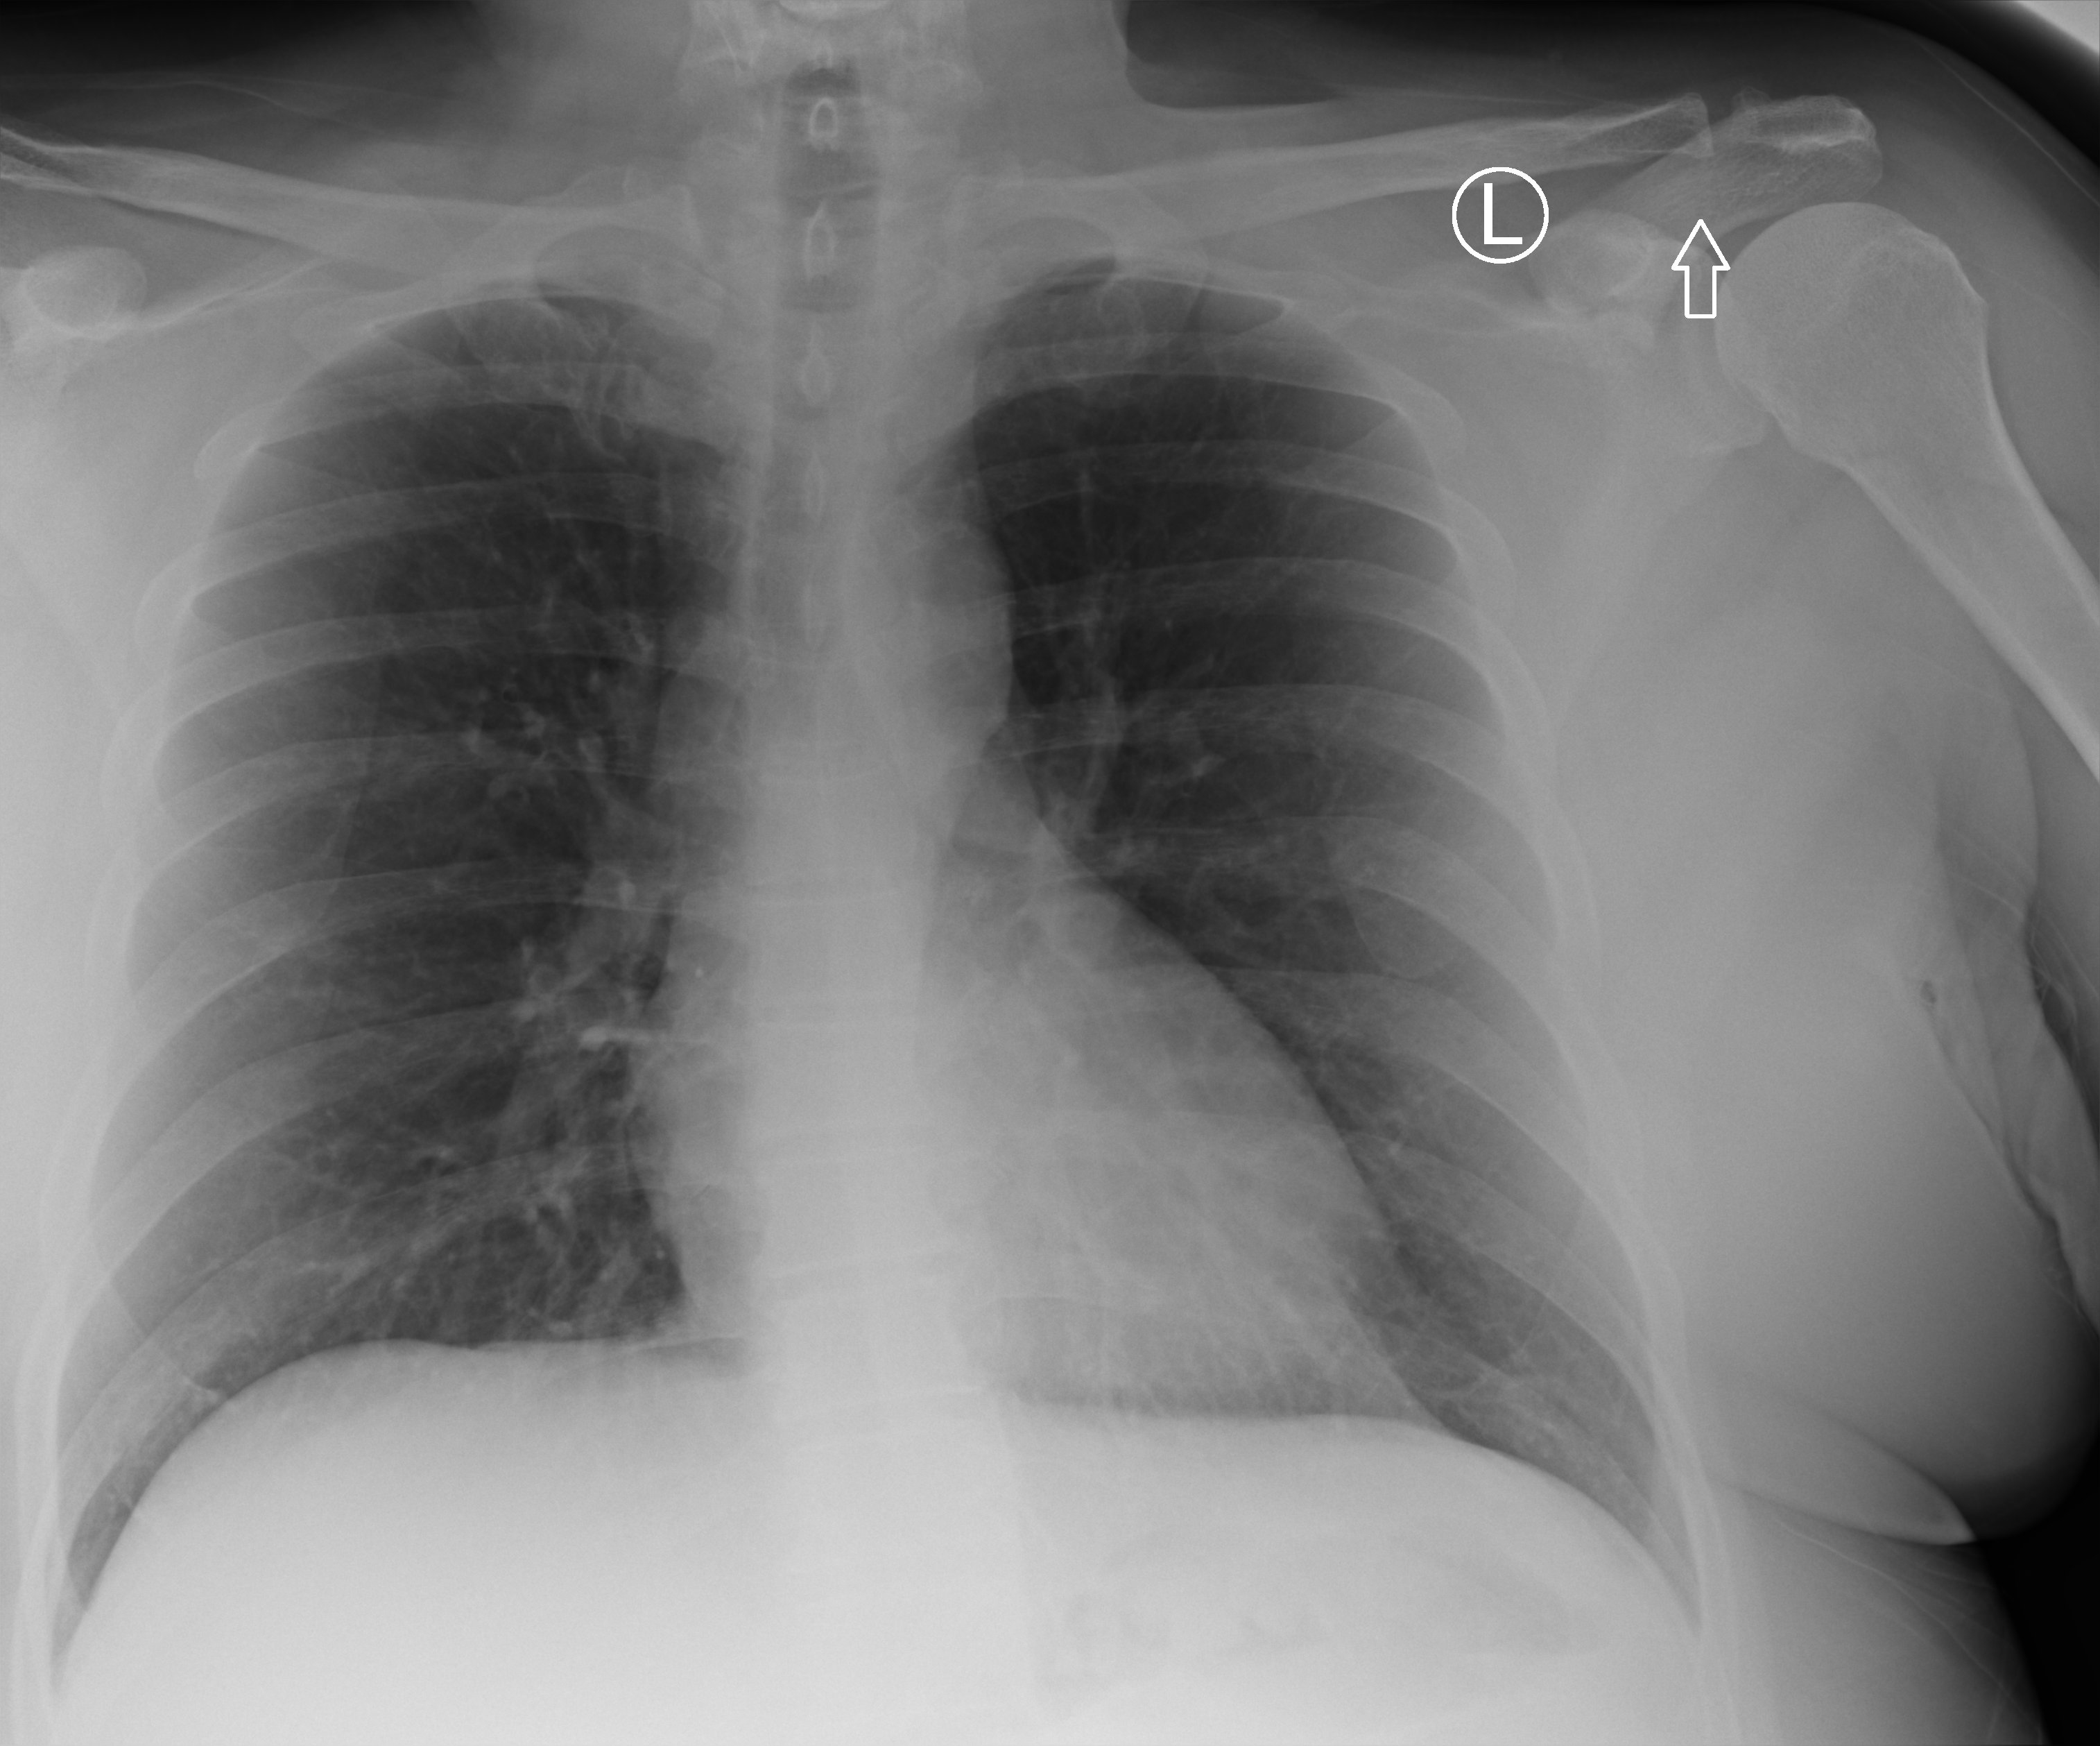
Portable chest radiograph; anteroposterior (AP) projection. Male patient hospitalised with COVID-19, age 60–74 years.
From the hospital-stay record, not from the radiograph (when in the stay this image was taken is not recorded): hypertension (admission record): no; length of hospital stay: 4 days; admitted to intensive care during this hospital stay: no.